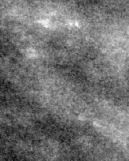
Crop from a digitized film mammogram around one marked abnormality, right breast, CC view, BI-RADS breast density category 1 (scale 1–4).
Marked abnormality: calcifications, morphology fine linear branching, distribution clustered / linear; BI-RADS assessment category 5; pathology result (as recorded, not read from the image): malignant.